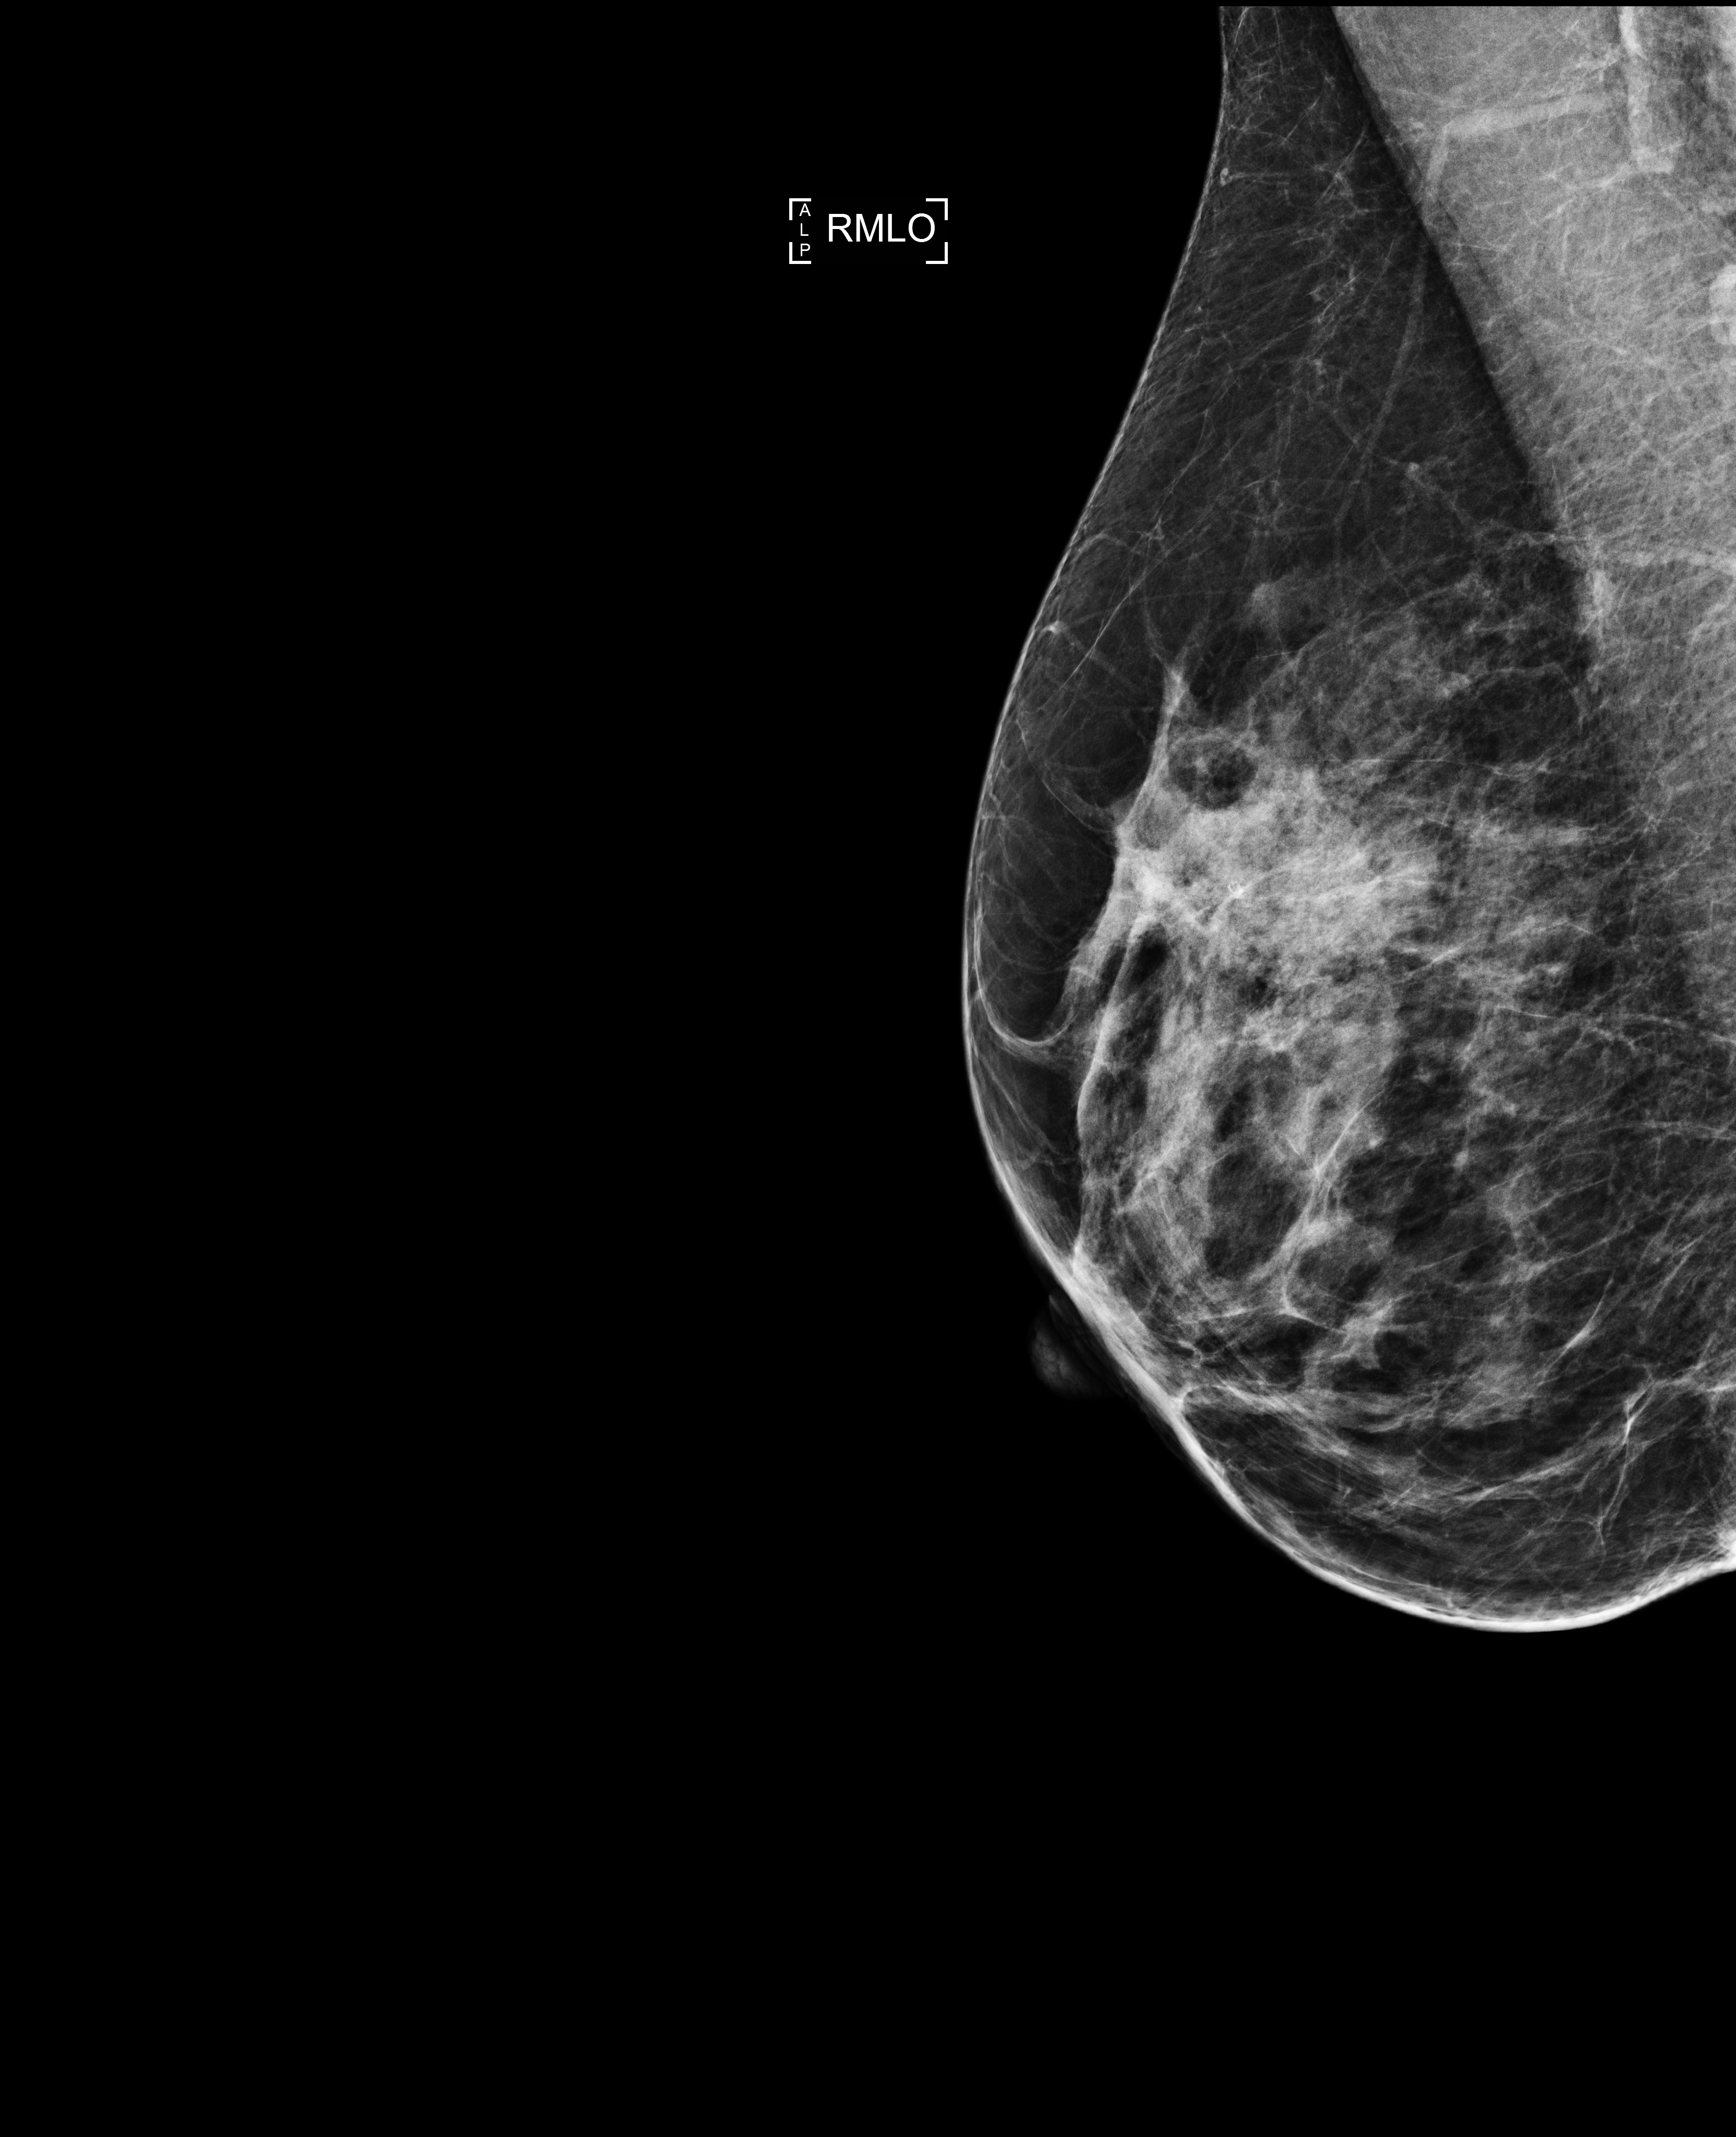
Full-field digital mammogram (FFDM), right breast, MLO view, annual screening mammography examination, compressed breast thickness 55 mm. Patient aged 57 years (female).
- BI-RADS breast density category at the screening exam (both breasts, scale 1–4): 3
- final BI-RADS category for the screening round (tomosynthesis exam, both breasts): category 1
- recall: no recall after this screen